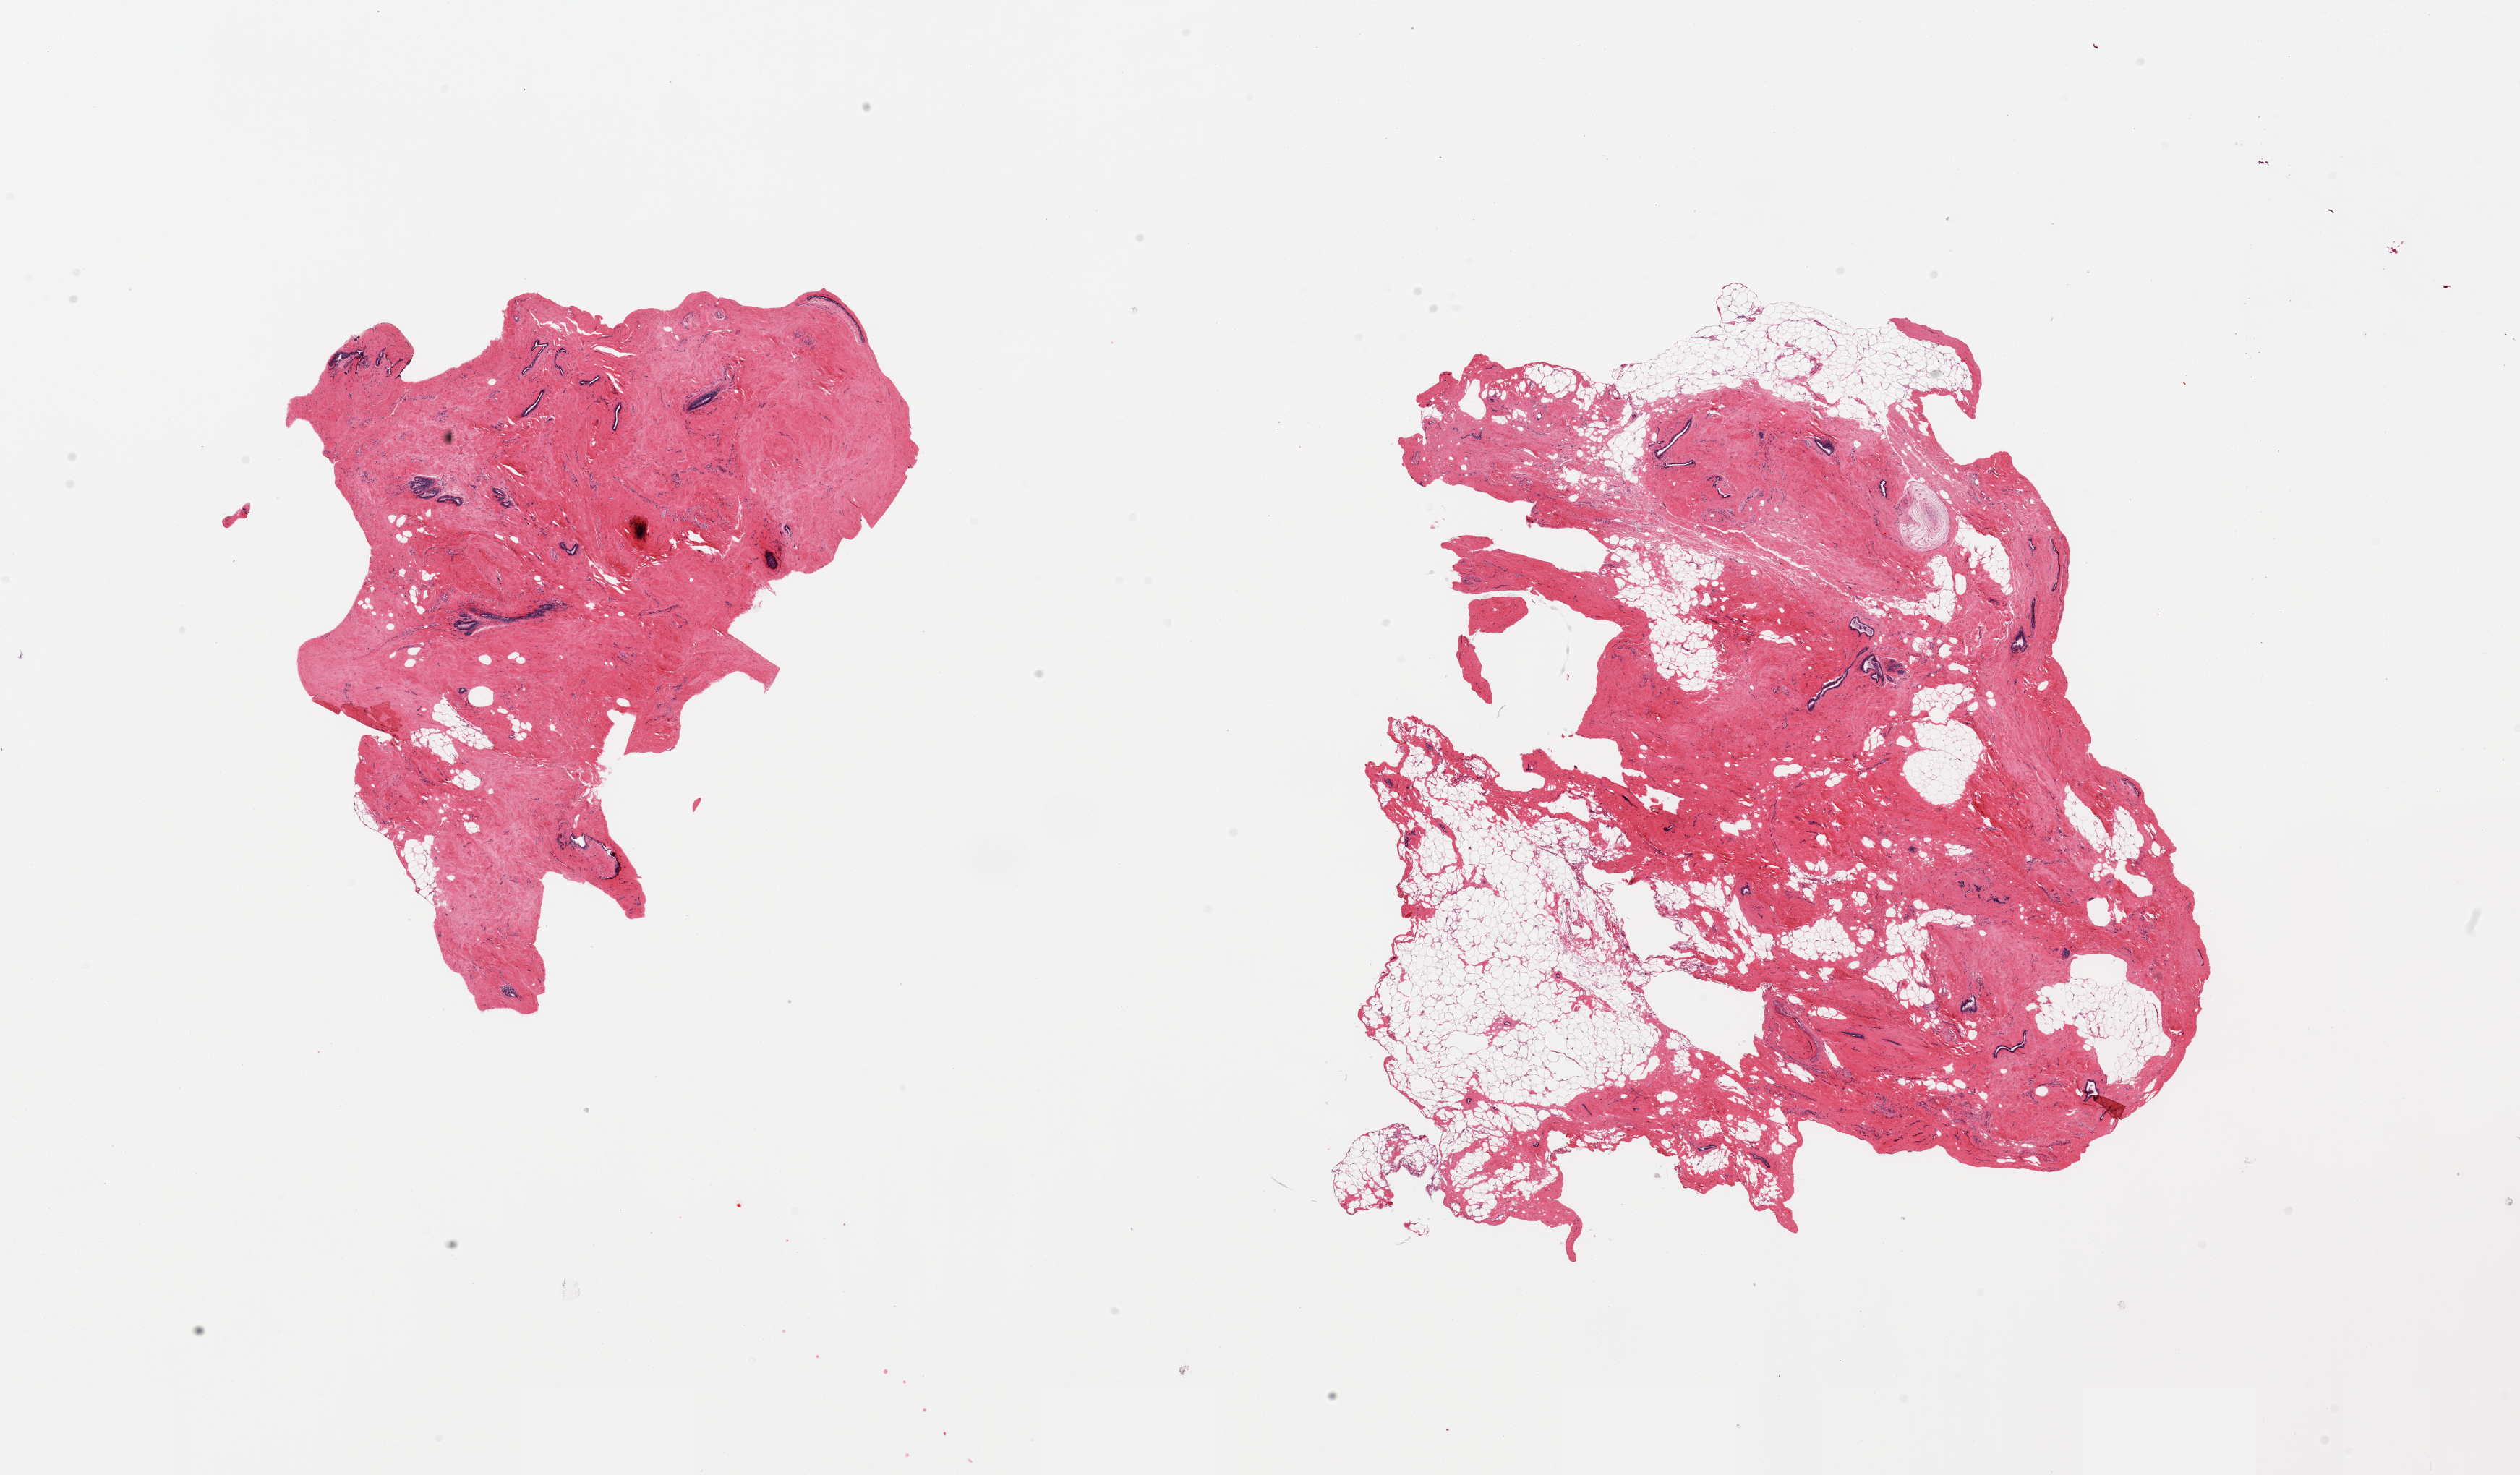
Digitized haematoxylin and eosin-stained section — shown as a low-resolution overview of the whole scanned area (about 27.6 x 16.1 mm, slide scanned at 20x). PAXgene-fixed paraffin-embedded (PFPE) section. Target tissue: breast. Donor tissue sample.
Review note (as recorded): 2 pieces gynecomastoid ductal and stromal hyperplasia; duct elements.